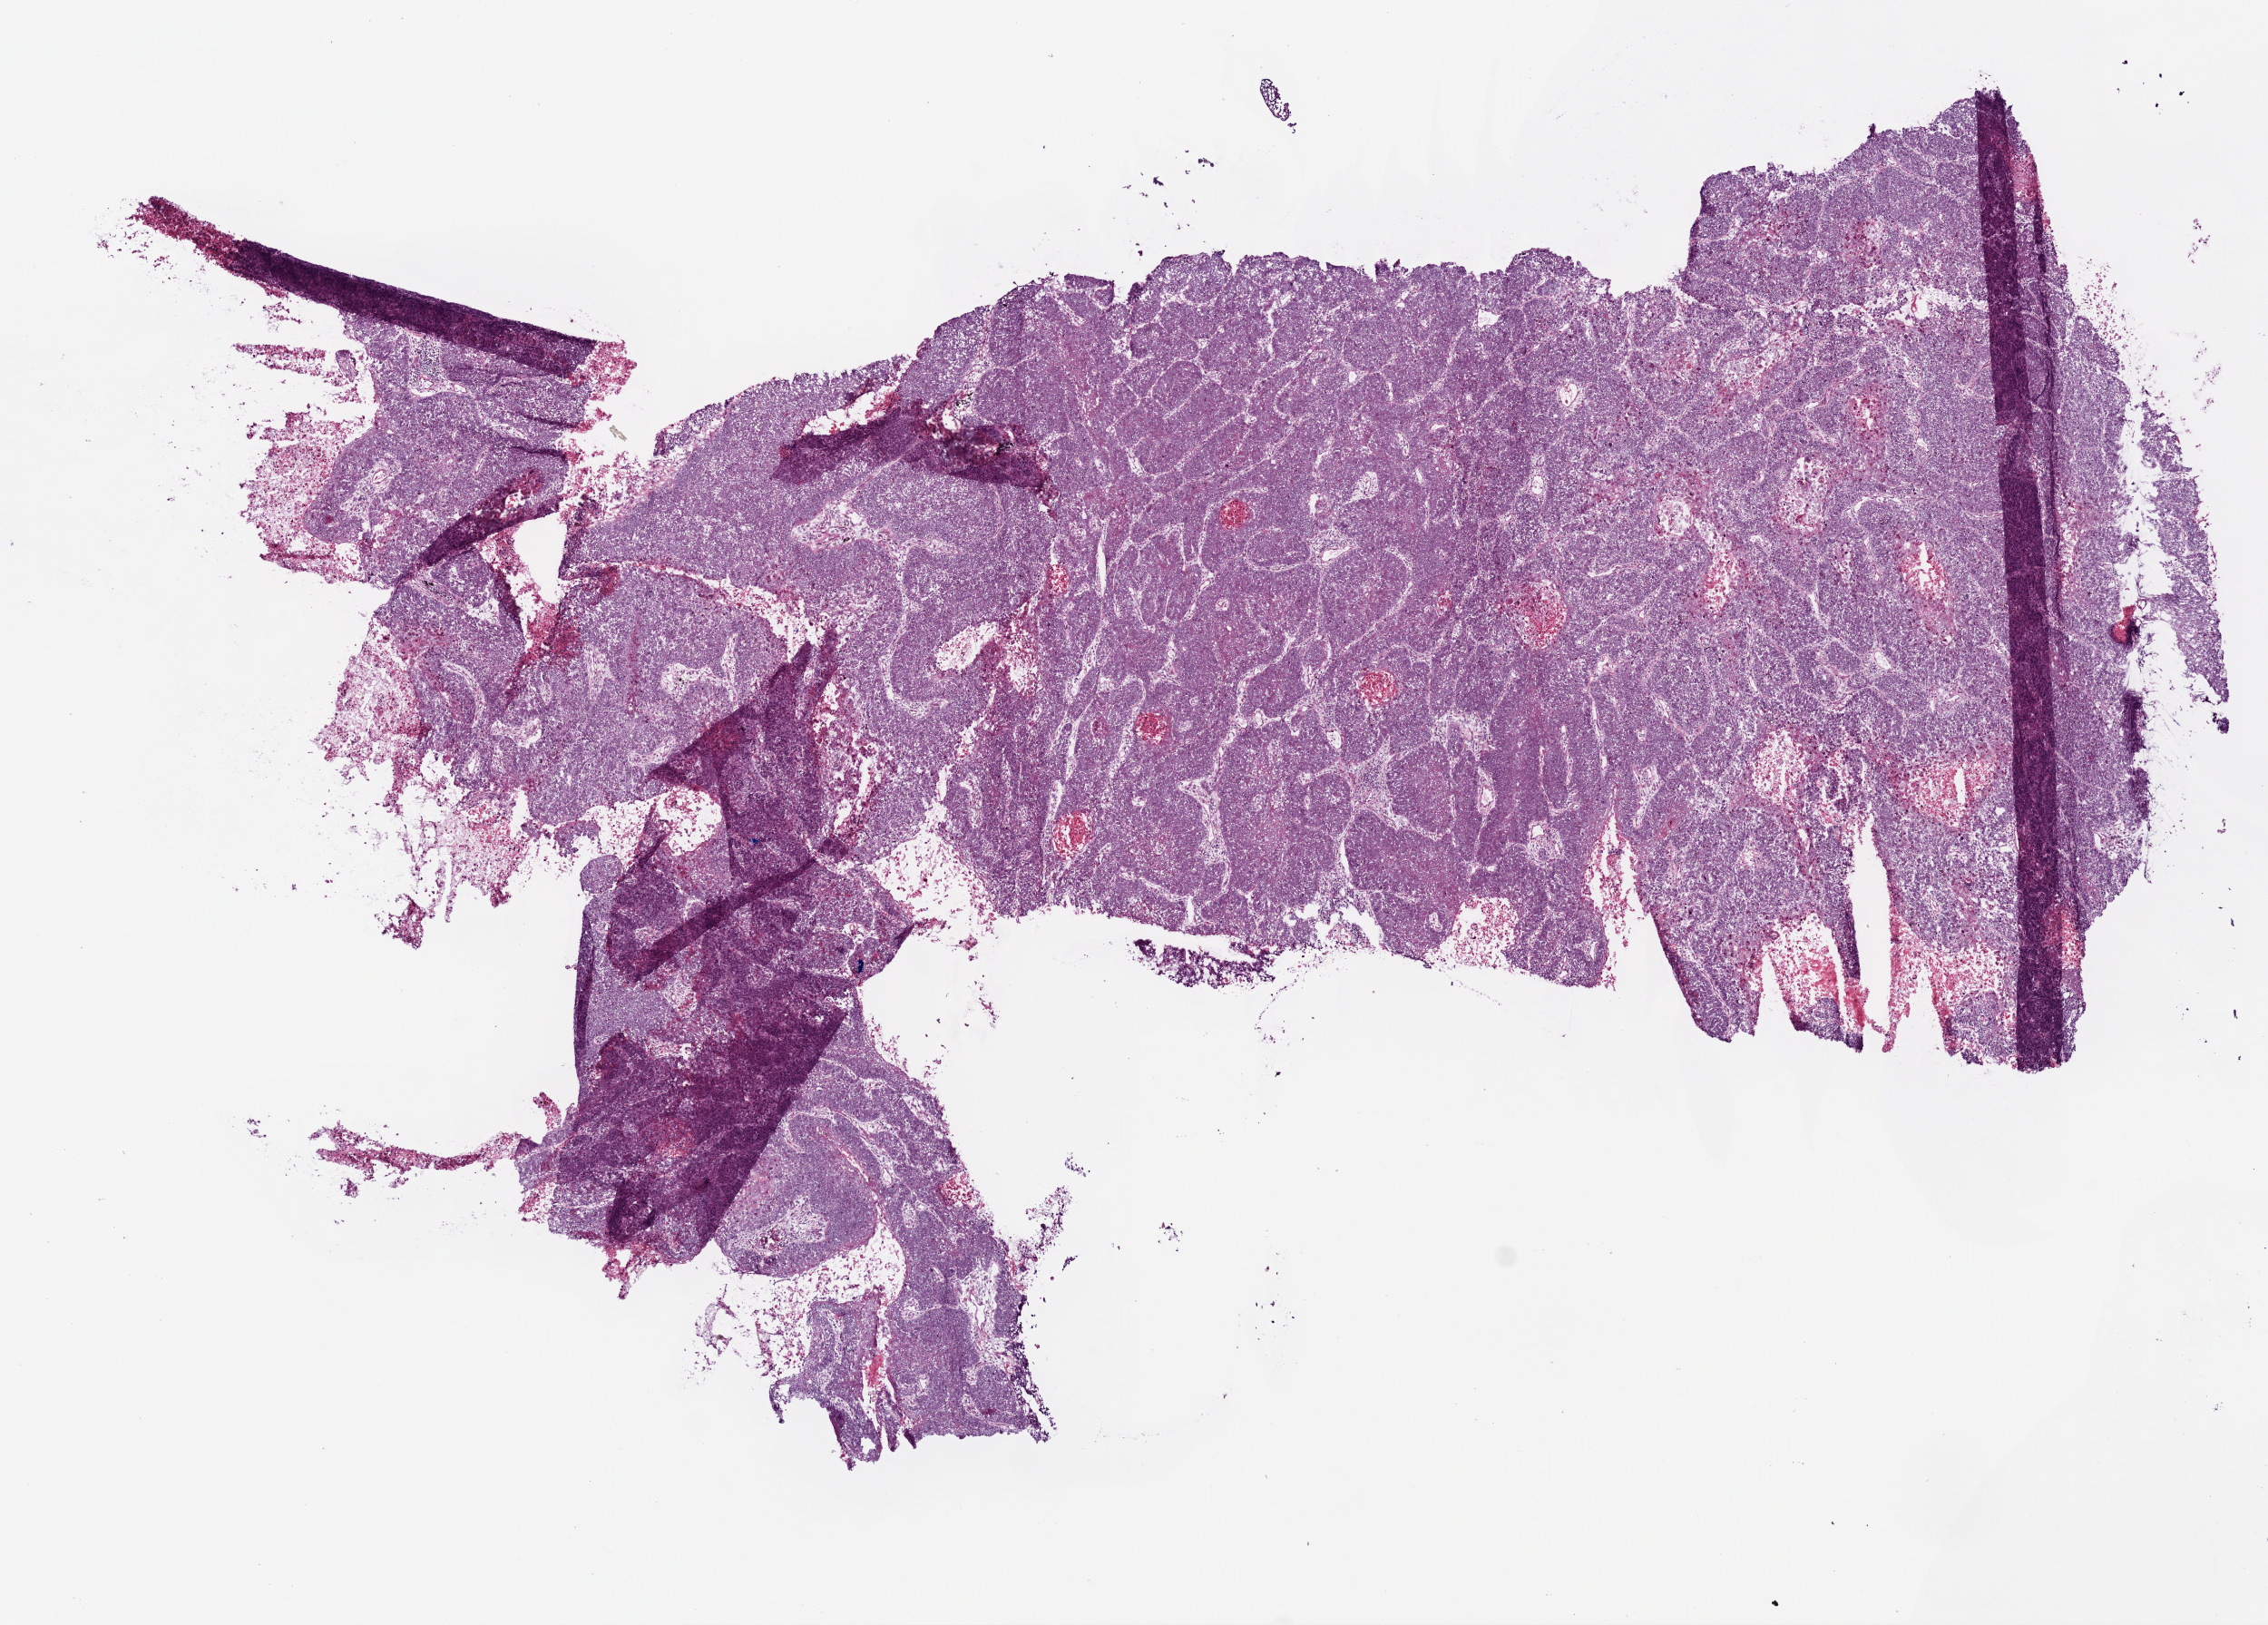
Whole-slide histology image, H&E-stained — shown as a low-resolution overview of the whole scanned area (about 10.0 x 7.2 mm, from a 20x scan). Frozen section. Primary tumour sample from the lung. Male, age 65 years at initial diagnosis. Slide review estimates, as recorded: tumour cells 85%, tumour nuclei 90%, normal cells 0%, stromal cells 5%, necrosis 10%.
TNM: T4 N1. AJCC pathologic stage: IIIB. Laterality: right. Diagnosis: Basaloid squamous cell carcinoma (upper lobe, lung).